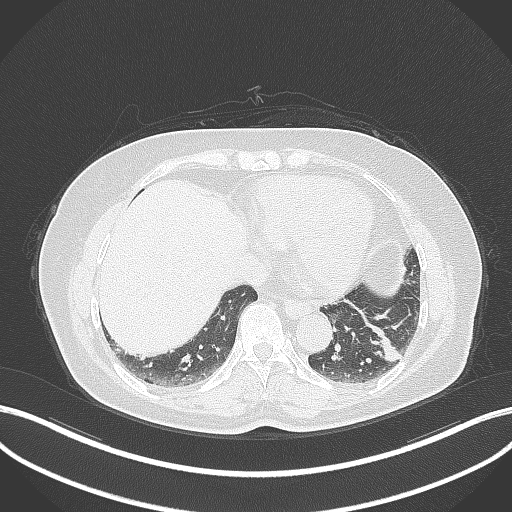
Chest CT, one axial slice. Slice 113 of 311 in the series (ordered by position). Lung window (W 1500 / L -600 HU). 1 mm slice thickness. 512 × 512 image matrix. Female patient, age 59 years. From the clinical record (not read from this slice): clinical TNM (as recorded): T2a N0 M0; histopathological grade: G2-3.
Outlined on this slice (rectangle marked by the reading radiologist):
- lung tumour (recorded histology: adenocarcinoma): bounding box [x1, y1, x2, y2] px = [369, 323, 405, 367]